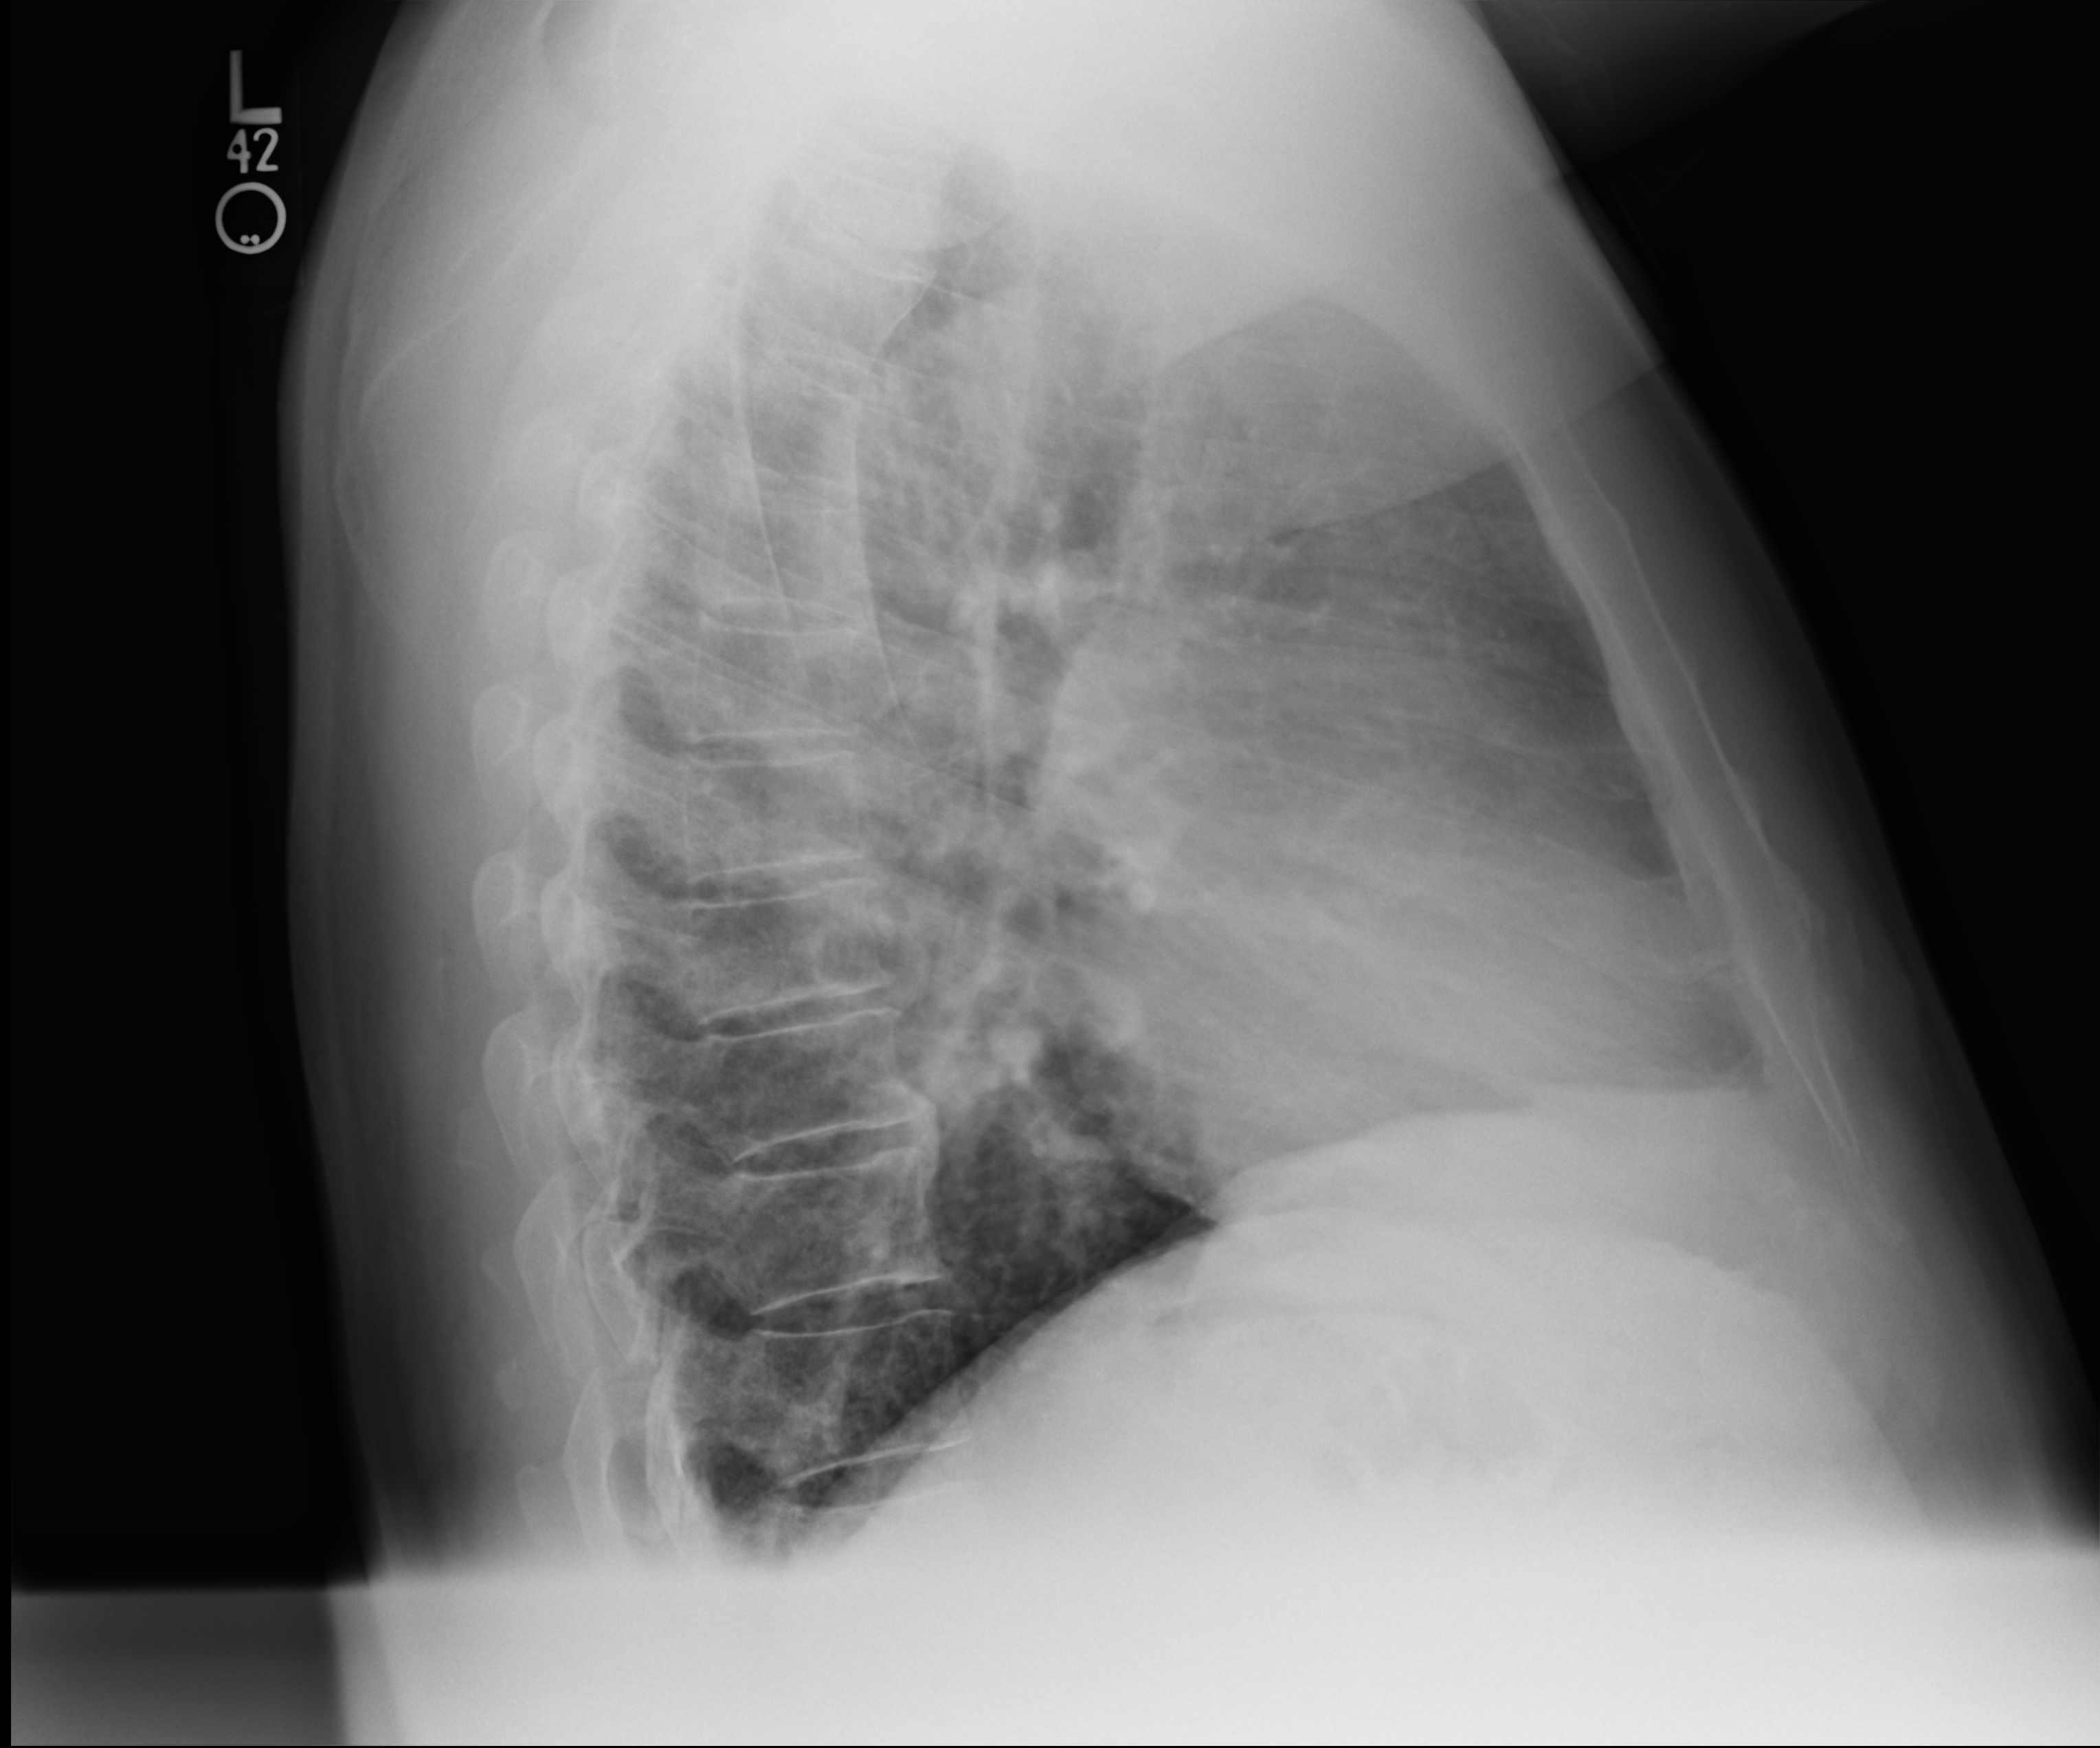
Chest radiograph, lateral projection. Patient hospitalised with COVID-19; male, aged 60–74 years.
Admission-level facts for this patient (not findings on this image; timing relative to this image not recorded): hypertension (admission record): yes.